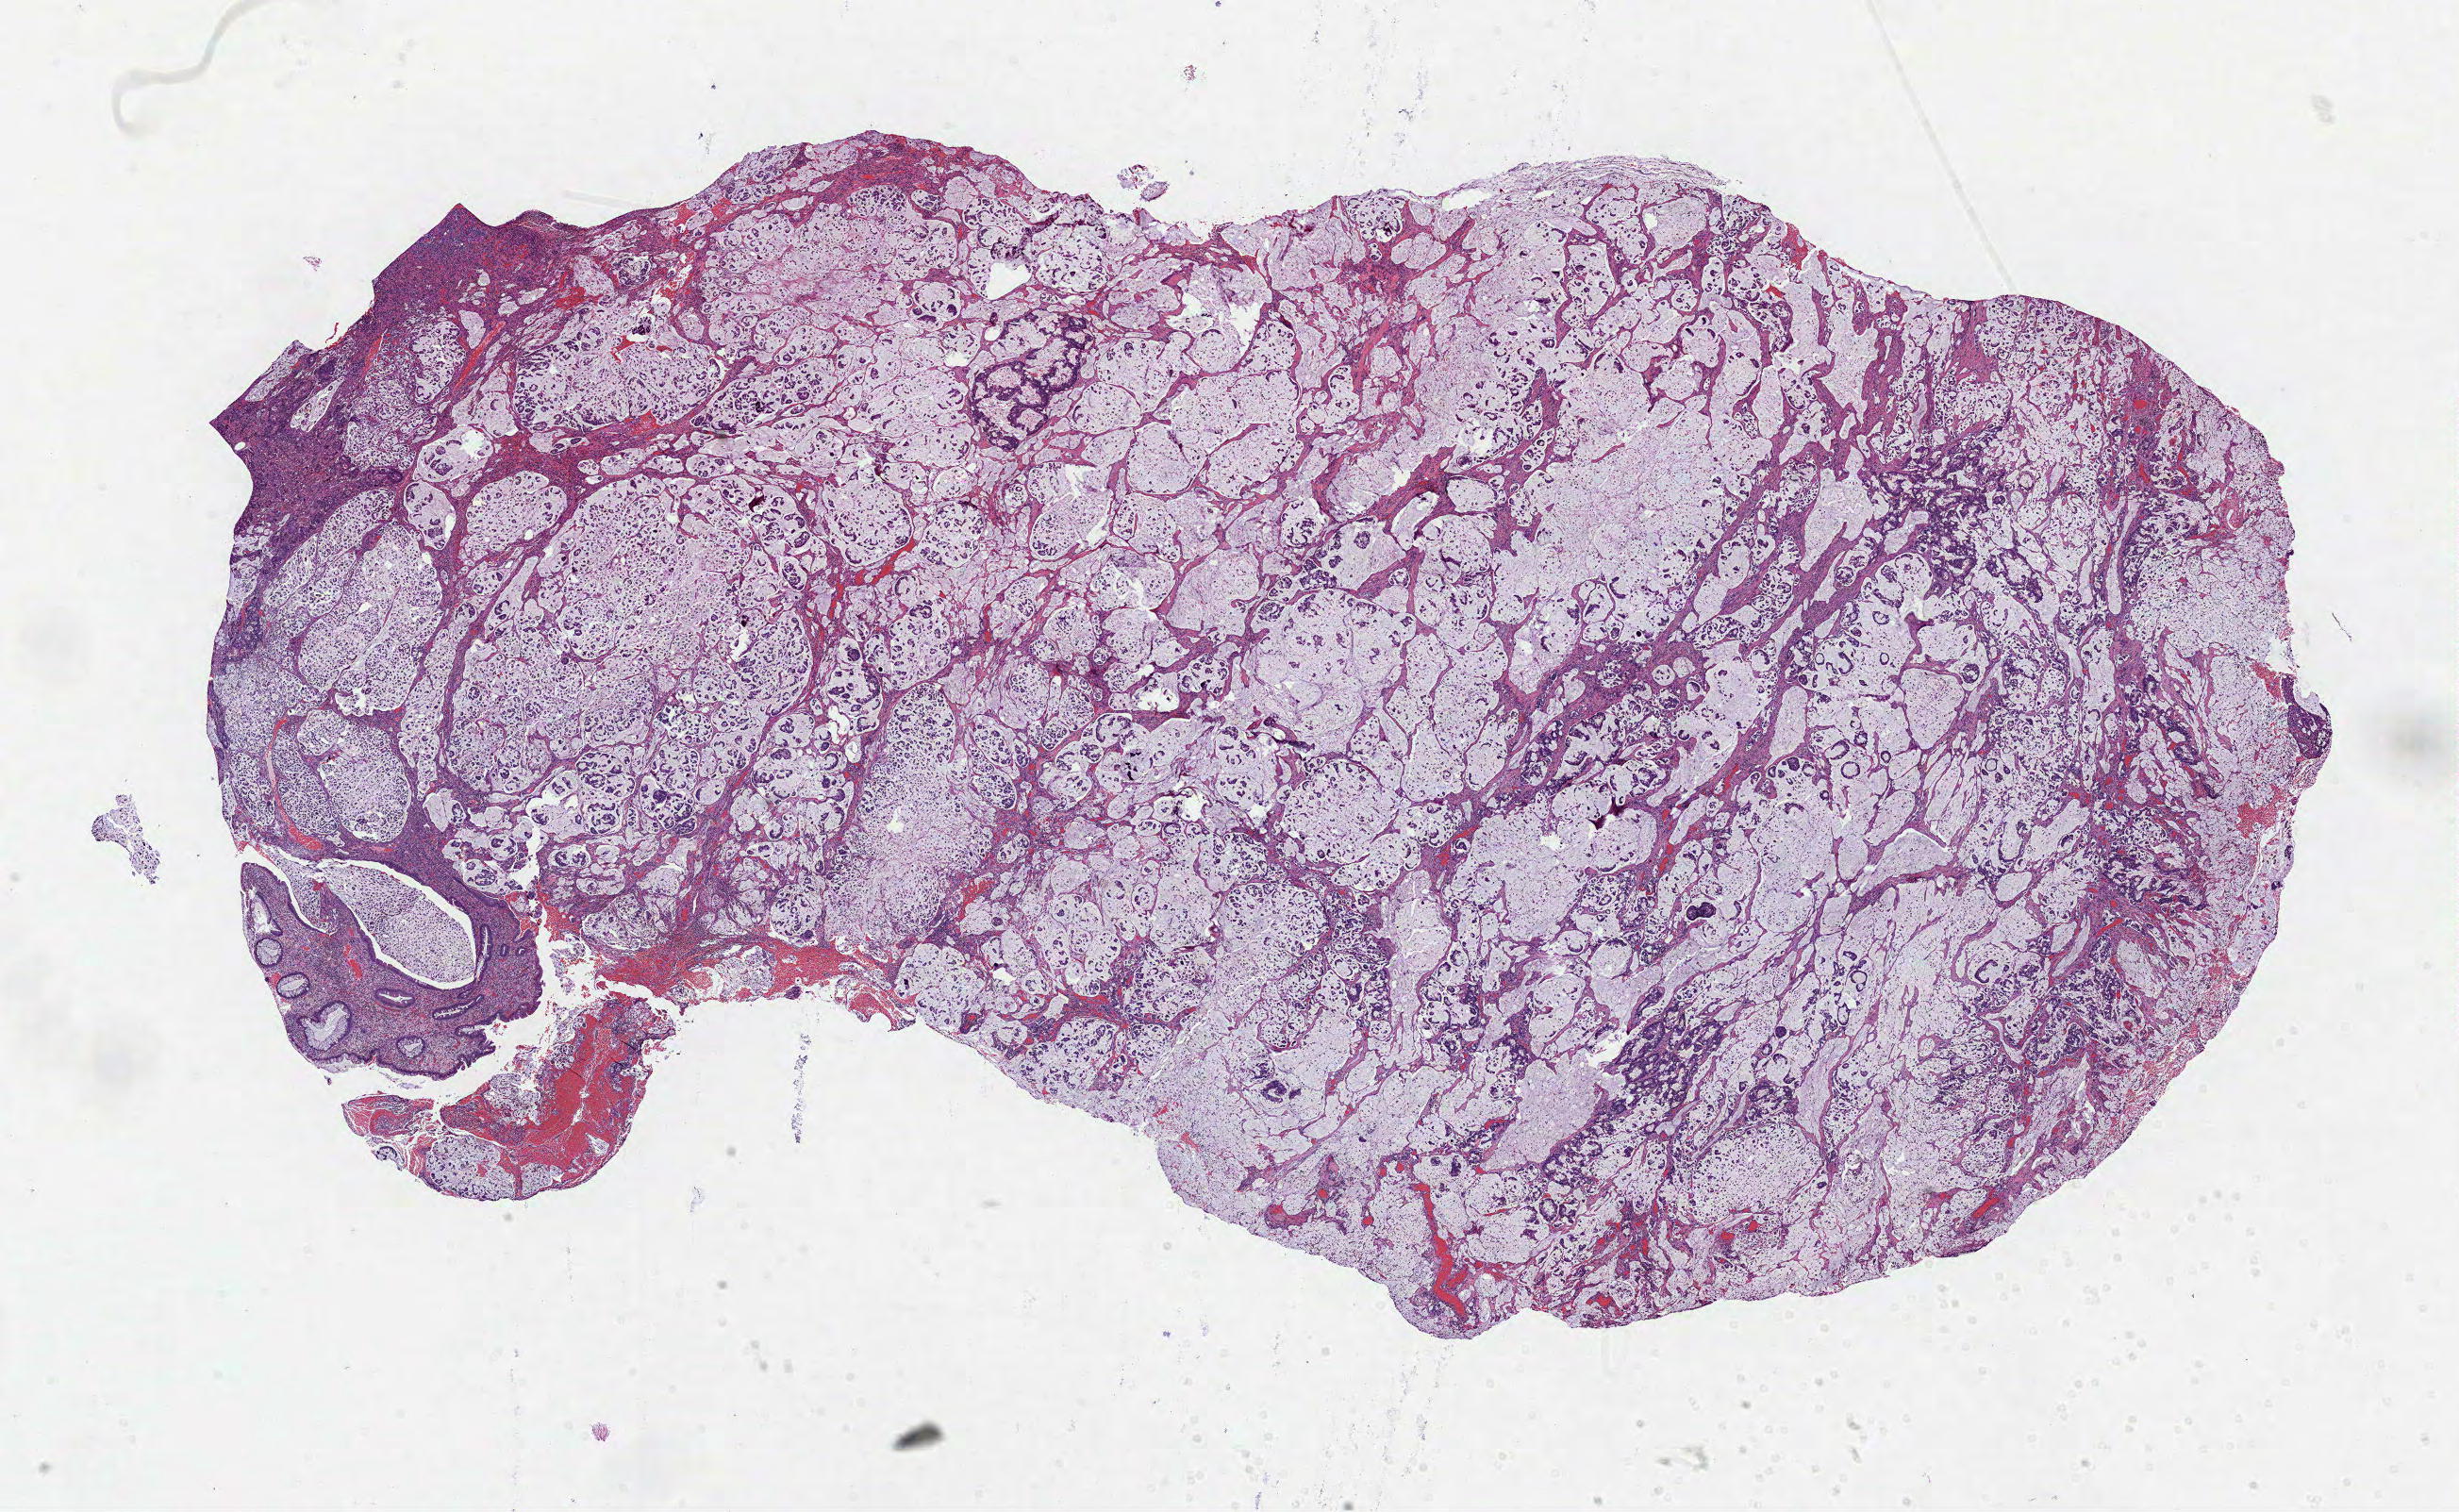
Whole-slide histology image, H&E, whole scanned area (about 21.0 x 12.9 mm, acquisition: 40x scan) shown as a low-resolution overview. FFPE section. Sample: primary tumour, rectum. Patient: male, age at initial diagnosis 54 years.
TNM: T3 N0 M0. Lymph nodes positive (case pathology): 0 of 32 examined. AJCC pathologic stage: IIA. Pathologic diagnosis: Mucinous adenocarcinoma (rectosigmoid junction).